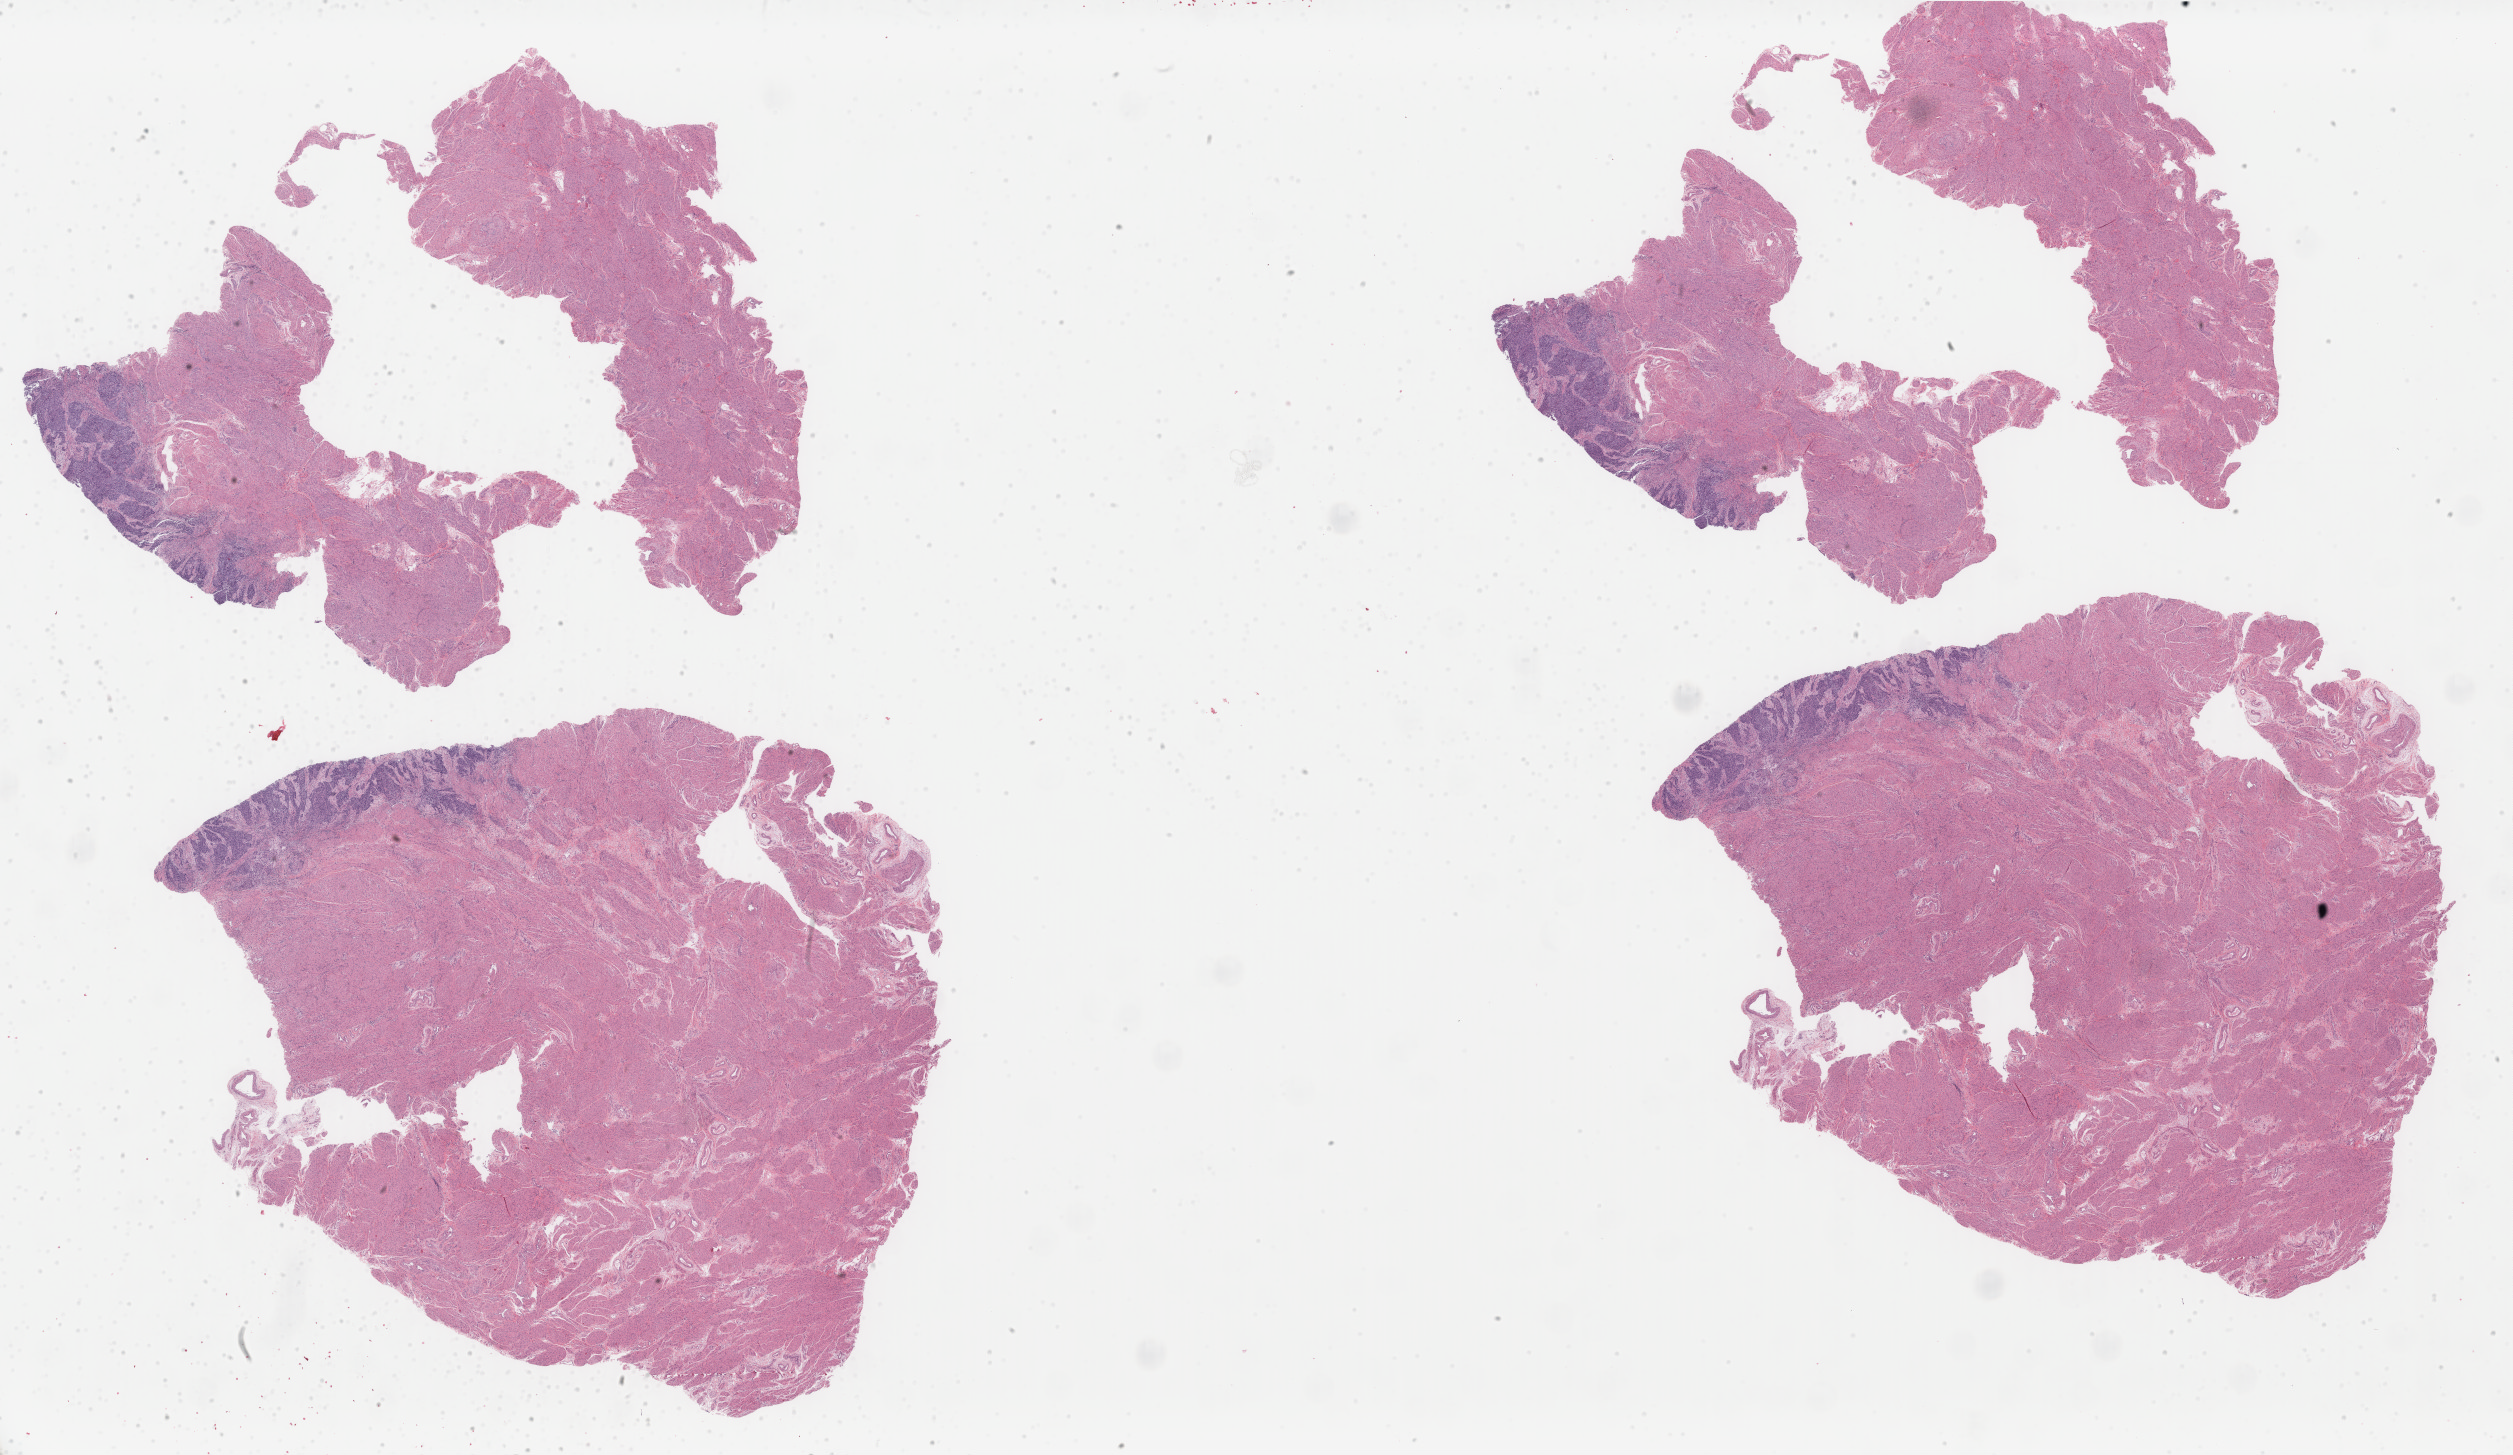
Whole-slide histology image, Hematoxylin and eosin (H&E) stained — low-resolution overview of the scanned area, about 39.9 x 23.1 mm (from a 40x scan). Formalin-fixed paraffin-embedded (FFPE) diagnostic section. Uterus, primary tumour sample. Female patient; age at initial diagnosis 67 years. Histologic grade: G3 (poorly differentiated).
Pathologic diagnosis: Endometrioid adenocarcinoma, NOS (endometrium). Lymph nodes positive (case pathology): 0 of 10 examined. FIGO stage: IB.